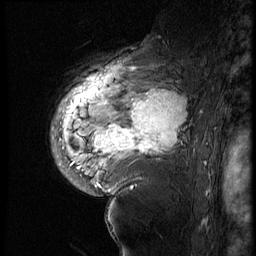
Breast MRI (dynamic contrast-enhanced), one sagittal slice. Position 45 of 60 along the scan axis. 4 images stored at this slice position (order not interpretable as contrast timing). 1.5 T. TE 4.2 ms, TR 9 ms. 256 × 256 image matrix, field of view 180 × 180 mm. Female patient, age 56 years. Case-level facts recorded for this patient, not image findings: setting: breast cancer imaged before/during neoadjuvant chemotherapy; receptor status: HER2-positive.
Structures marked on this image (semi-automatic segmentation, software-assisted and operator-edited):
- analysis volume of interest (the breast-tissue region the enhancement analysis was run in; not a lesion): box from (x=82, y=83) to (x=199, y=177) px
- tumour enhancement mask (voxels above the 140 % enhancement threshold inside the analysis volume of interest): (x=100, y=90)–(x=186, y=157)